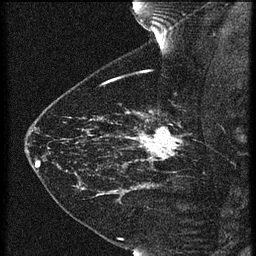
Breast MRI (dynamic contrast-enhanced), one sagittal slice. Position 48 of 60 along the scan axis. 3 images stored at this slice position (order not interpretable as contrast timing). 1.5 T. TE 4.2 ms, TR 21.3 ms. 1.5 mm slice thickness. 256 × 256 image matrix, field of view 180 × 180 mm. Patient: female, 43 years. Case-level facts recorded for this patient, not image findings: setting: breast cancer imaged before/during neoadjuvant chemotherapy; receptor status: HER2-positive.
Annotated regions visible in this slice (semi-automatically segmented with operator editing):
- analysis volume of interest (the breast-tissue region the enhancement analysis was run in; not a lesion): box from (x=119, y=114) to (x=189, y=173) px
- tumour enhancement mask (voxels above the 90 % enhancement threshold inside the analysis volume of interest): (x=126, y=128)–(x=182, y=161)